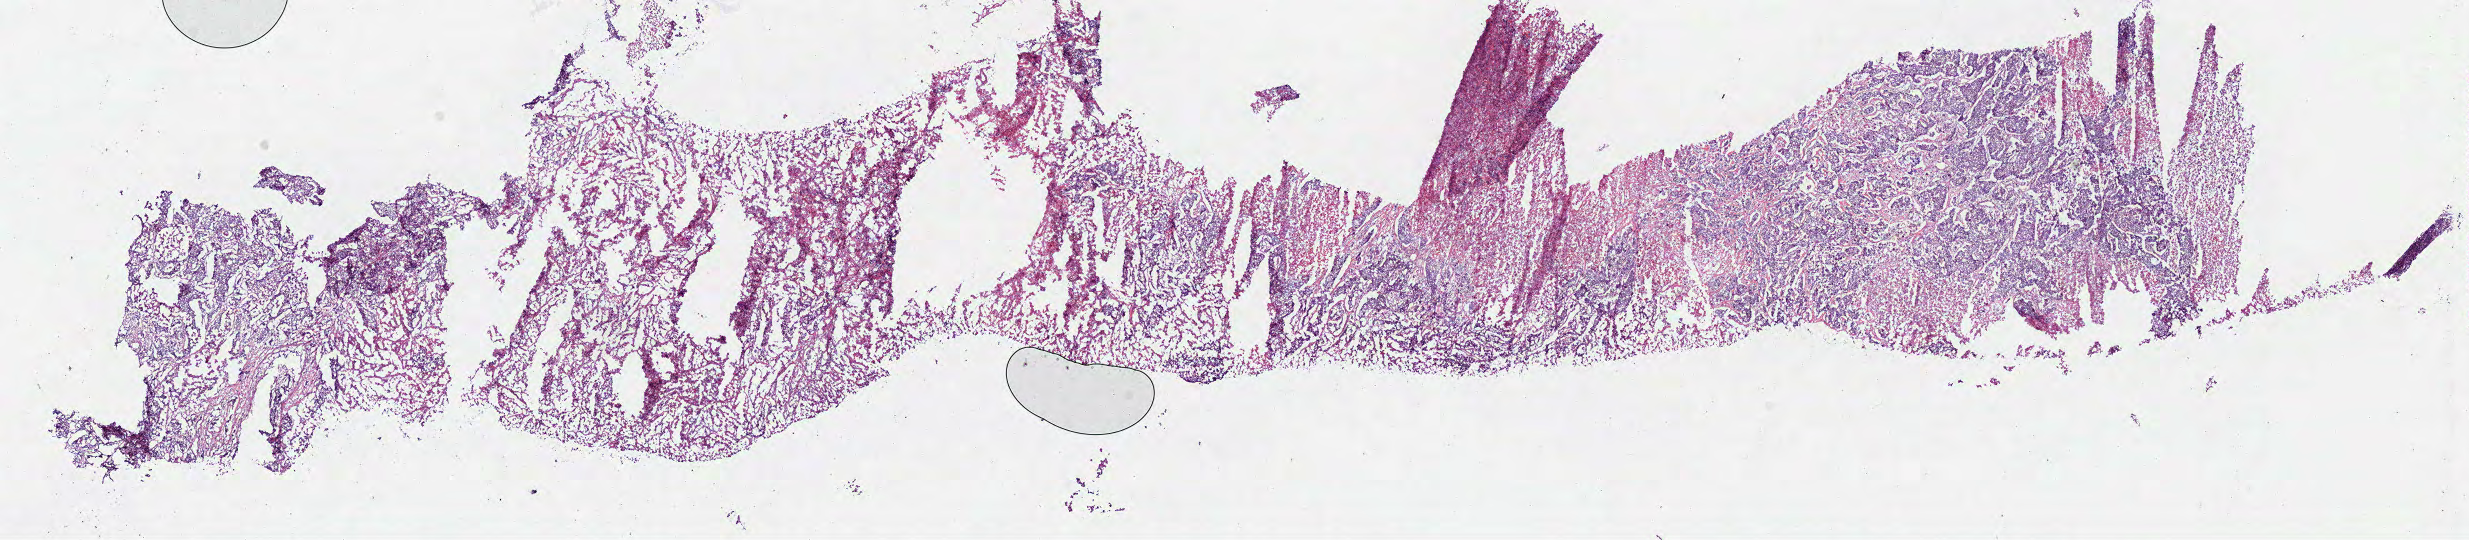
Hematoxylin and eosin (H&E) stained whole-slide image — whole scanned area (about 19.5 x 4.3 mm) shown as a low-resolution overview. Frozen section. Lung, primary tumour sample. Male patient; age at initial diagnosis 71 years. Slide review estimates, as recorded: tumour cells 60%, tumour nuclei 80%, normal cells 0%, stromal cells 10%, necrosis 30%.
AJCC pathologic stage: IIIA (6th edition). Laterality: right. TNM: T2 N2 M0. Histologic diagnosis: Squamous cell carcinoma, NOS (upper lobe, lung).